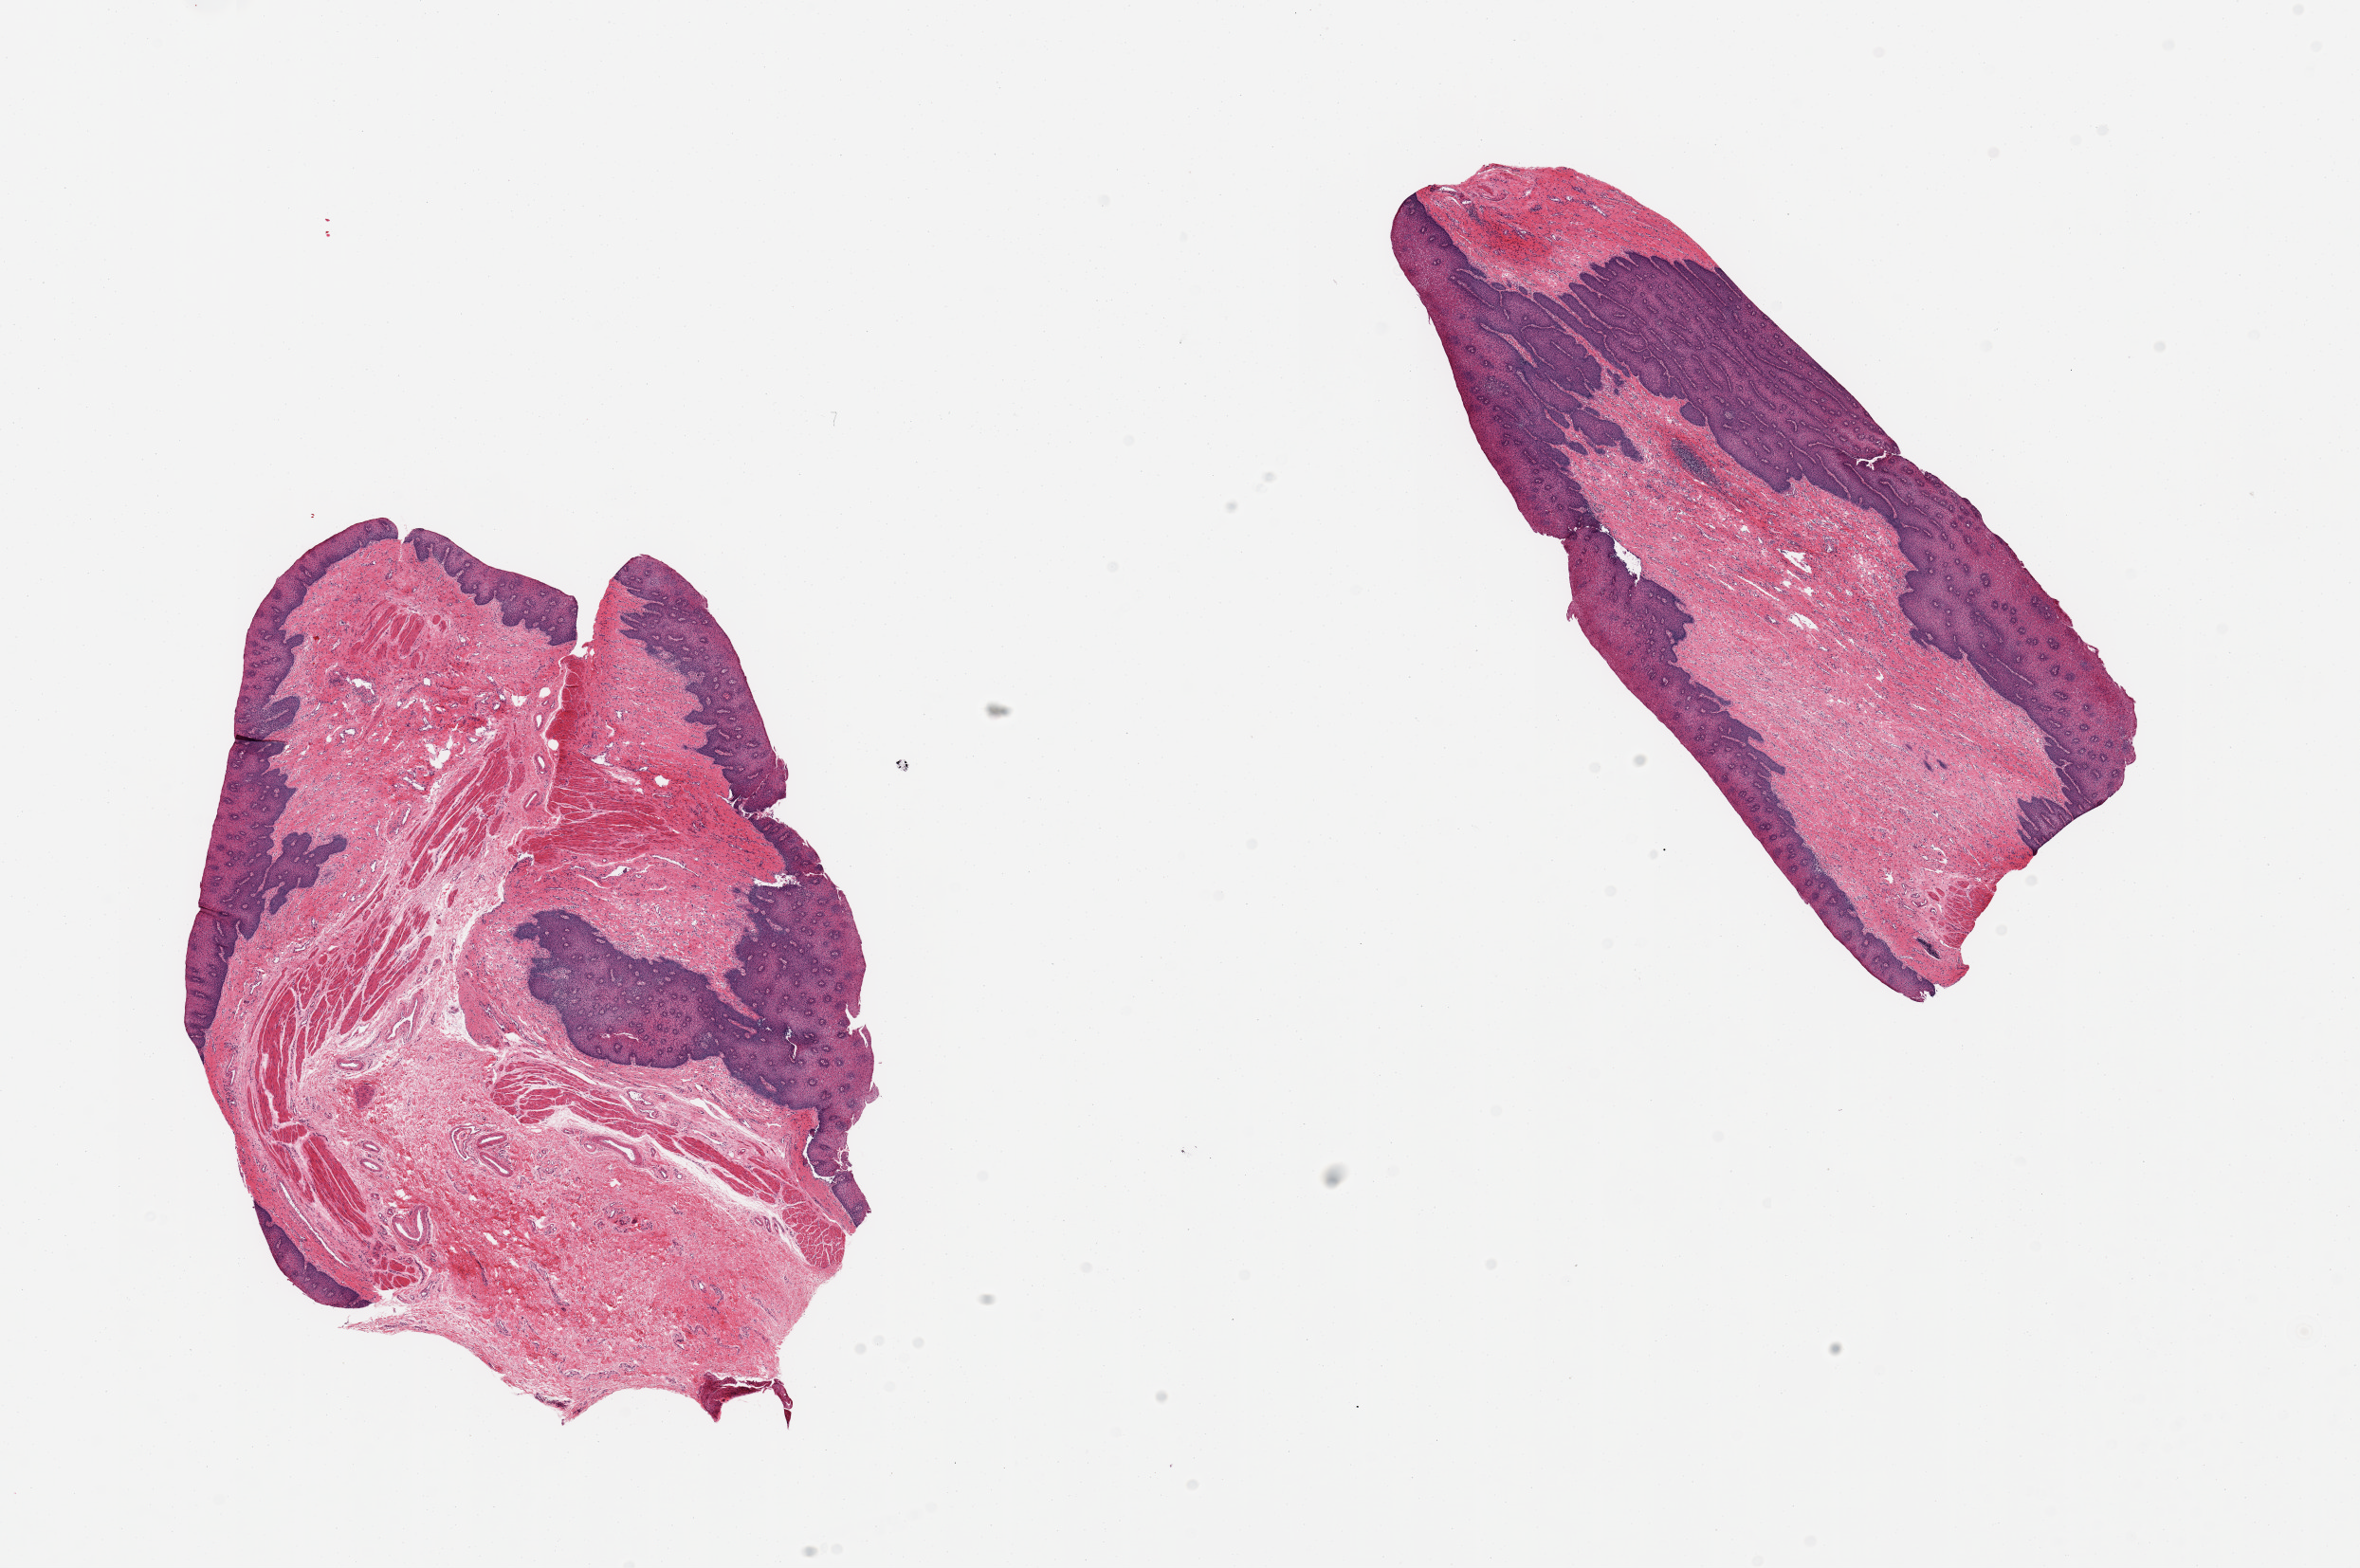
Digitized hematoxylin and eosin (H&E)-stained section, shown as a low-resolution overview of the whole scanned area (about 19.7 x 13.1 mm). PAXgene-fixed paraffin-embedded (PFPE) section. Sampled site (target tissue): esophageal mucous membrane. Donor tissue sample. Donor: male.
• review note (as recorded): 2 pieces; esophageal mucosa NOT prostate